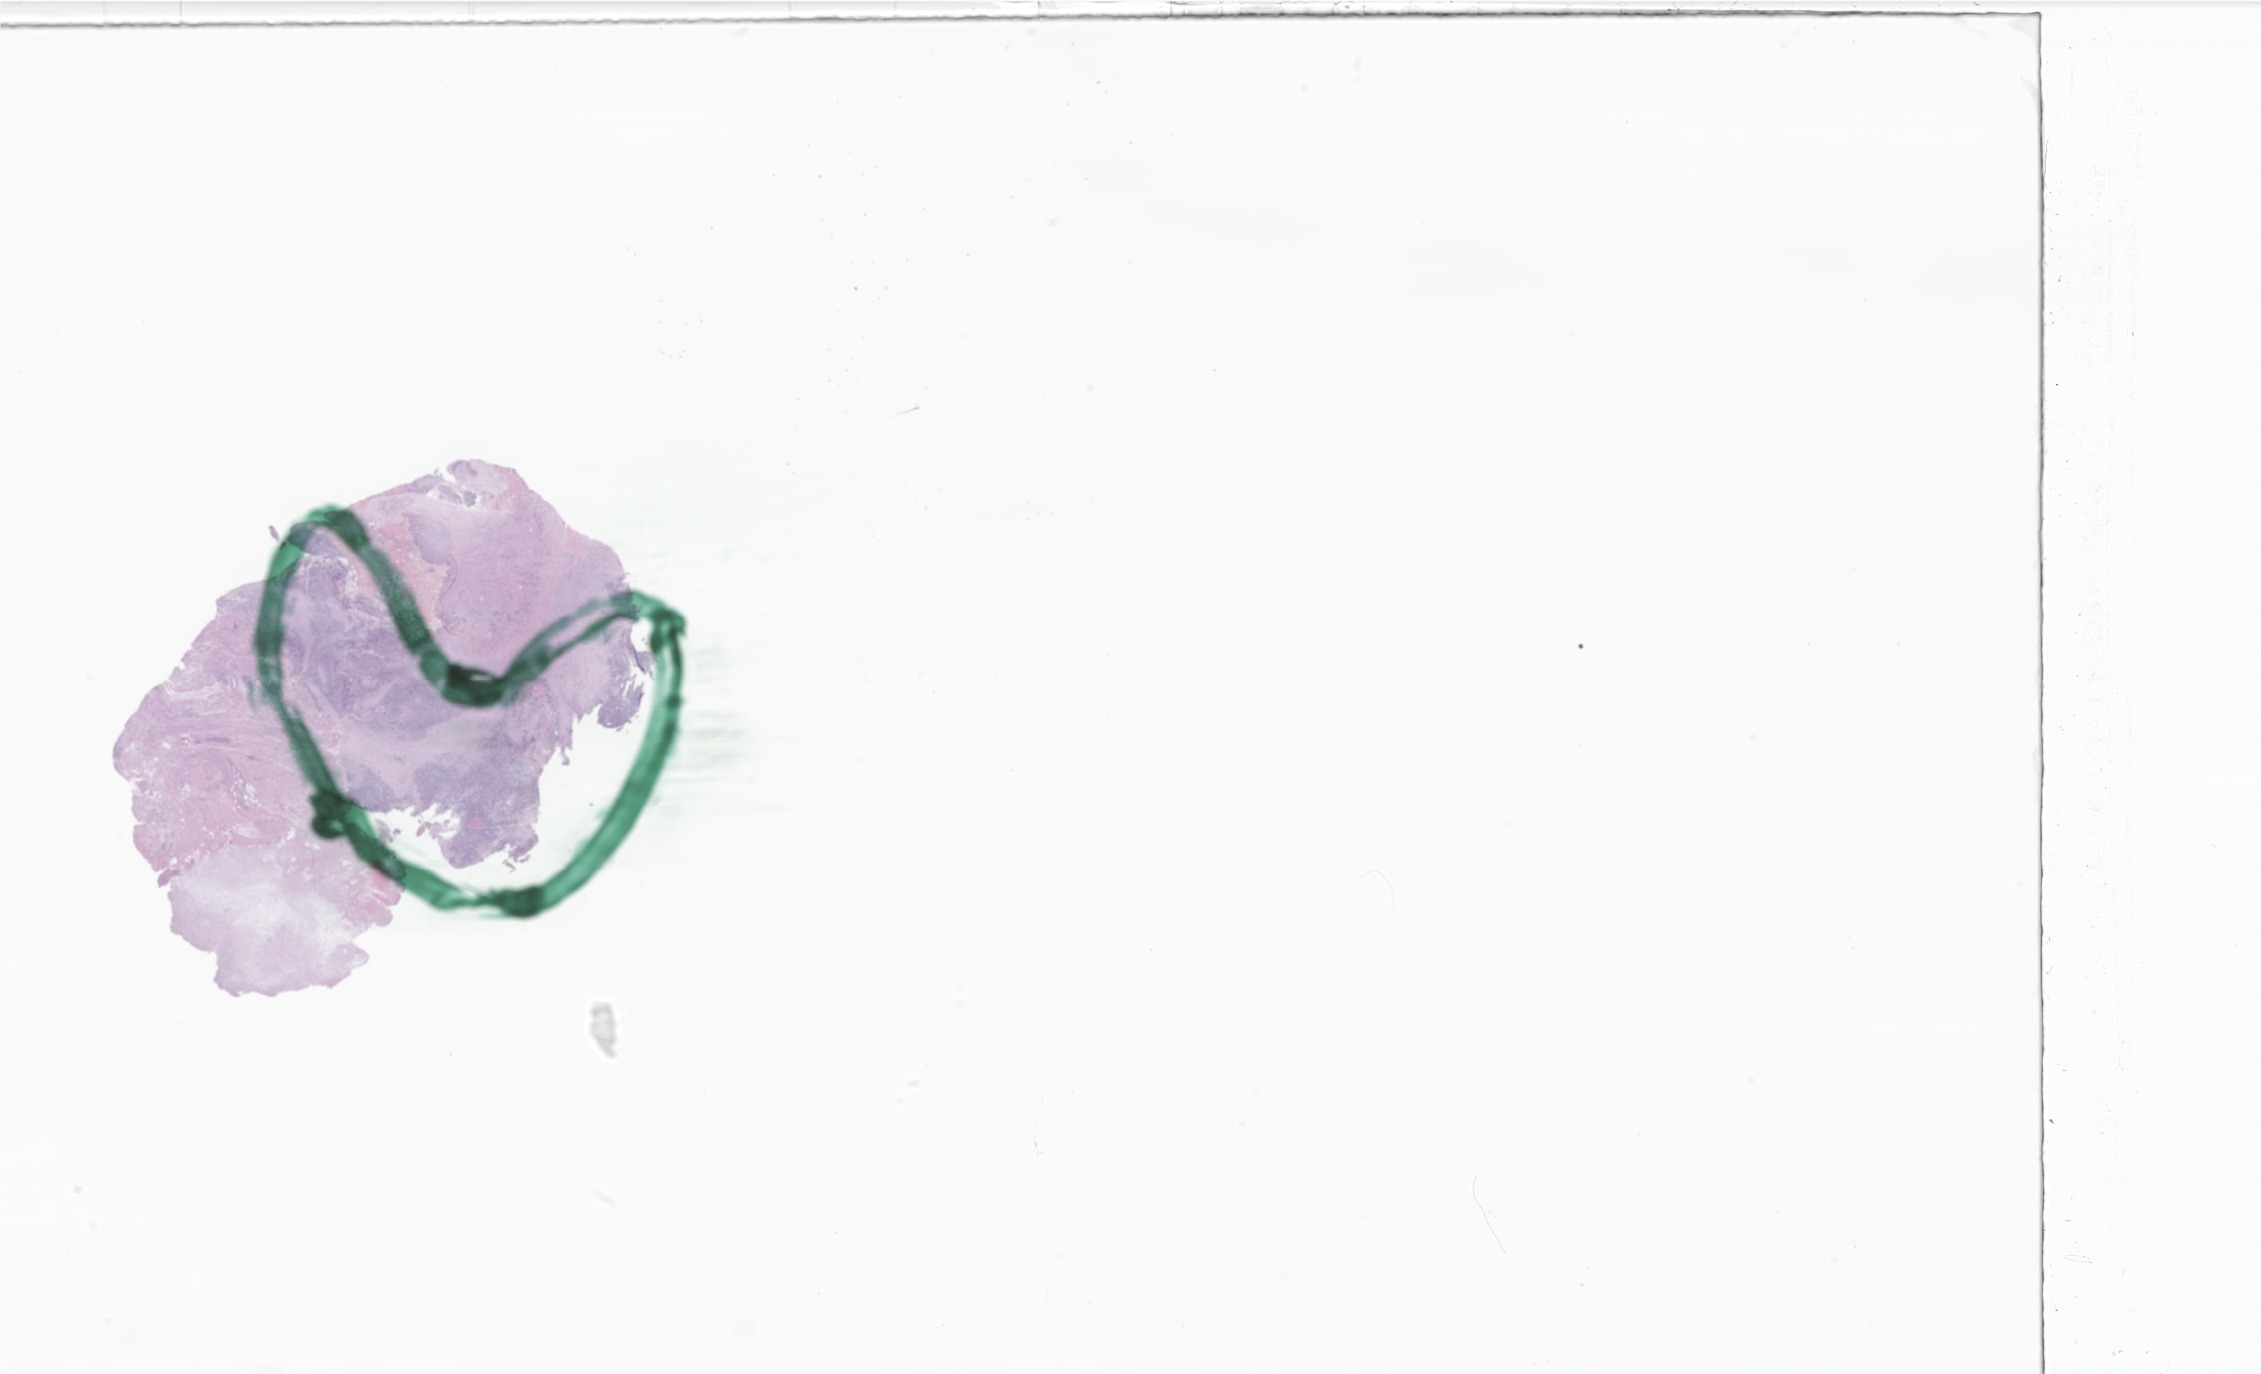
Digitized H&E-stained section of tumor tissue from the soft tissue of pelvis, a low-resolution overview of the entire scanned area, about 38.1 x 23.2 mm, formalin-fixed, paraffin-embedded (FFPE) tissue. Male patient, age 114 months (9 years 6 months).
* diagnosis: Sarcoma, NOS
* tissue or organ of origin (case record): connective, subcutaneous and other soft tissues of pelvis